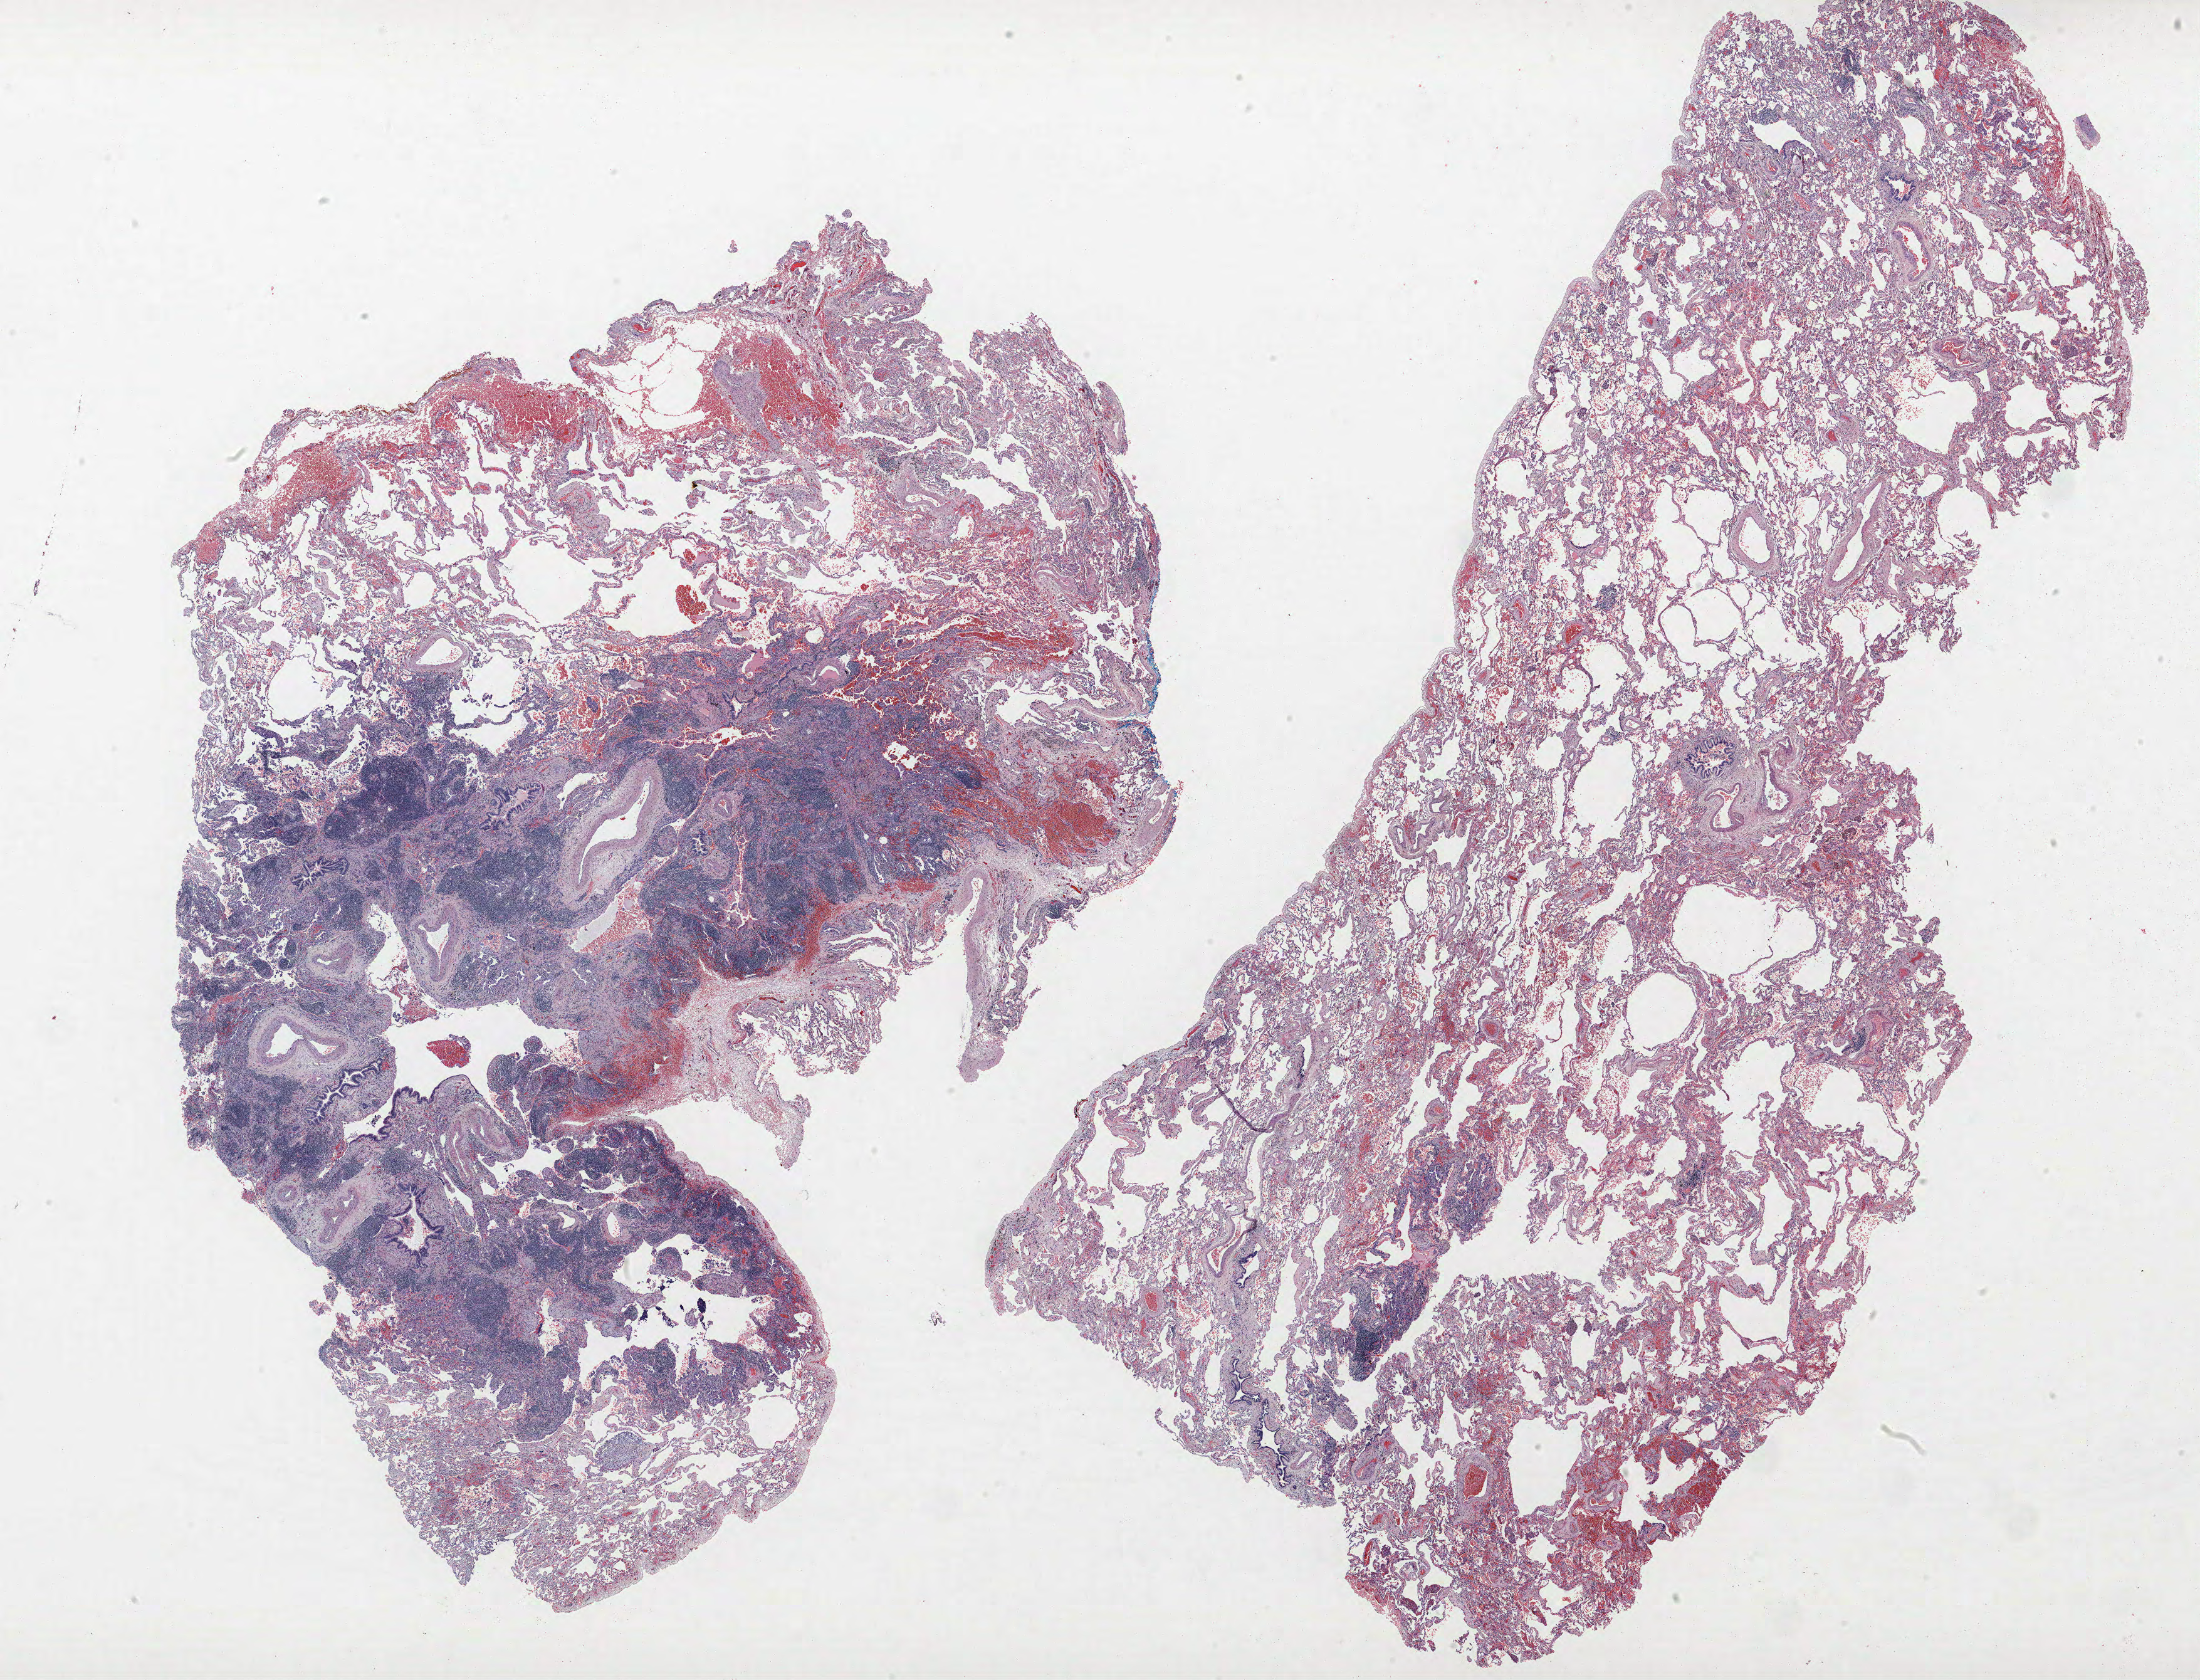
Whole-slide histology image, H&E — whole scanned area (about 28.1 x 21.4 mm) shown as a low-resolution overview, formalin-fixed paraffin-embedded (FFPE) section, lung. Female, age 59 at enrolment. Grade: moderately differentiated (G2).
• participant's lung-cancer diagnosis: Adenocarcinoma, NOS
• primary tumour location (clinical record): right middle lobe
• stage (AJCC 6th edition): IA
• tumour size (pathology): 11 mm
• note: participant had 2 primary lung cancers recorded; fields above describe the first